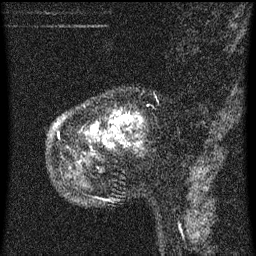
Breast MRI (dynamic contrast-enhanced), one sagittal slice. Position 16 of 60 along the scan axis. Dynamic contrast-enhanced series, image 2 of 3 at this slice position (ordered by acquisition). 1.5 T. TE 4.2 ms, TR 8 ms. 2 mm slice thickness. 256 × 256 image matrix, field of view 180 × 180 mm. Female patient, age 55 years.
Outlined on this slice (semi-automatically segmented with operator editing):
- analysis volume of interest (the breast-tissue region the enhancement analysis was run in; not a lesion): box from (x=48, y=96) to (x=149, y=155) px
- tumour enhancement mask (voxels above the 70 % enhancement threshold inside the analysis volume of interest): (x=58, y=112)–(x=142, y=141)